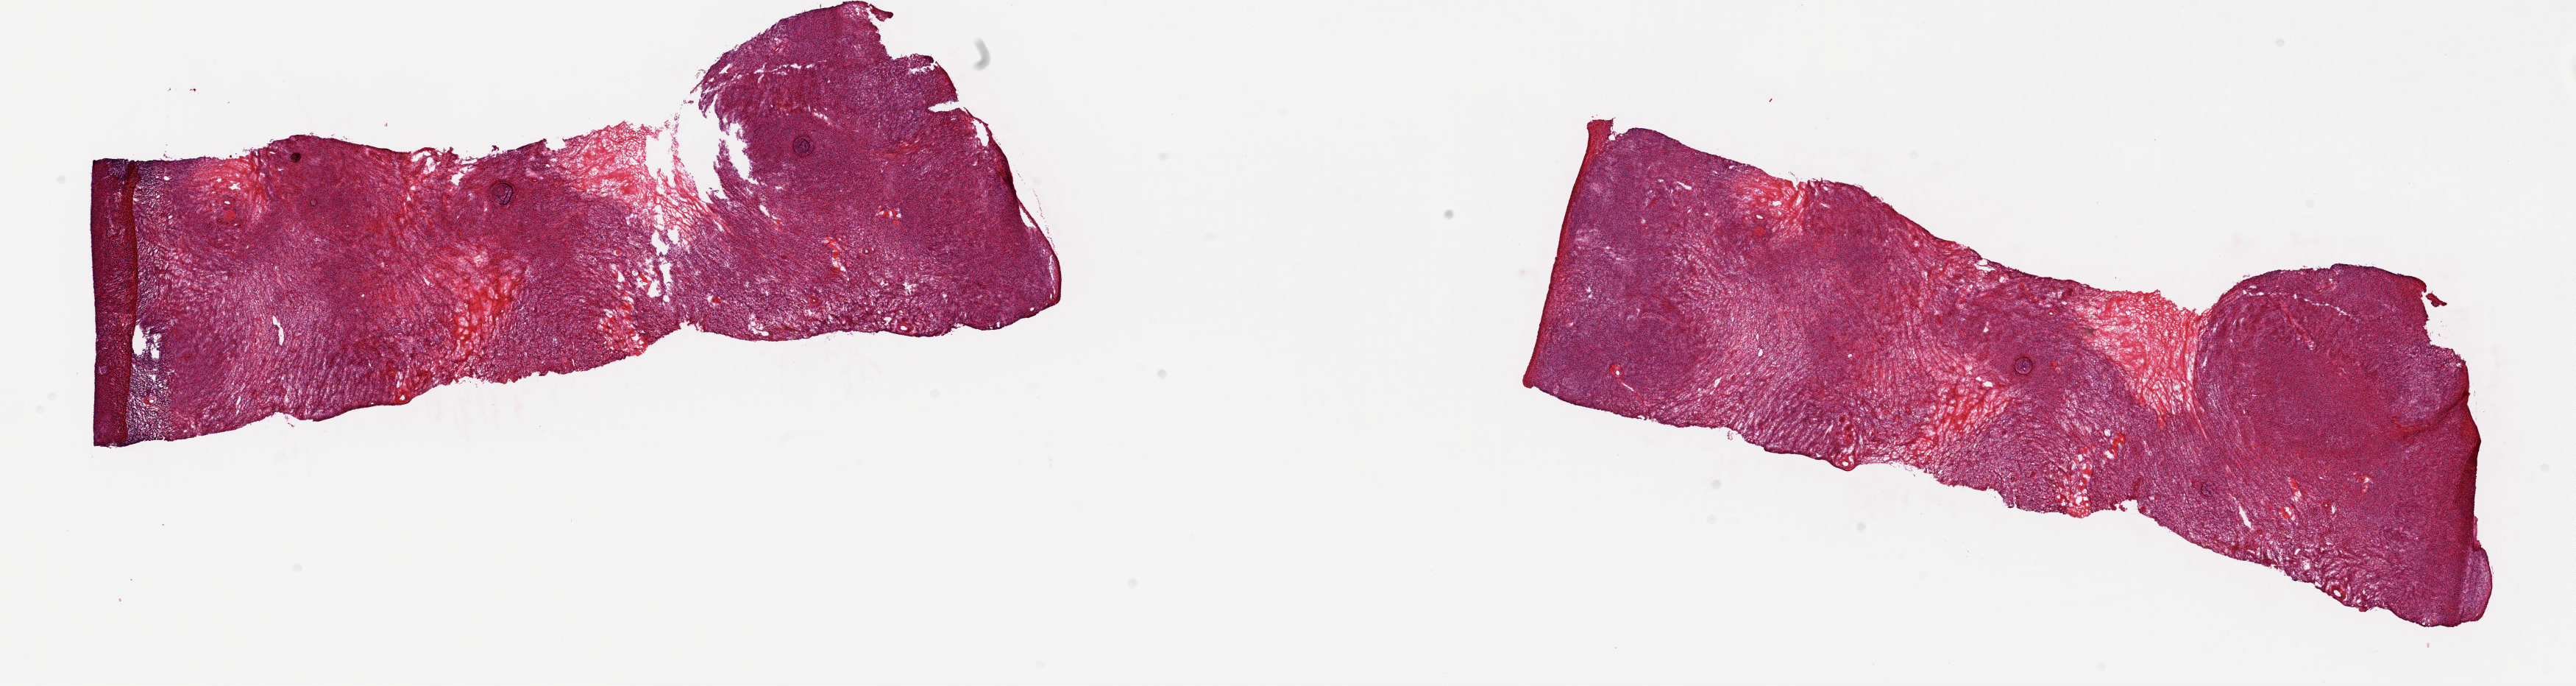
H&E-stained whole-slide image, shown as a low-resolution overview of the whole scanned area (about 27.8 x 7.4 mm); frozen section from the top of the tissue portion; solid tissue normal (non-tumour tissue) sample from the uterus. Female patient; age at initial diagnosis 58 years. Slide review estimates, as recorded: tumour cells 0%, tumour nuclei 0%, normal cells 80%, stromal cells 20%, necrosis 0%. Inflammatory infiltration, as recorded: lymphocyte infiltration 40%, monocyte infiltration 20%, neutrophil infiltration 20%.
- this section: solid tissue normal sample (biorepository sample class)
- patient diagnosis: Endometrioid adenocarcinoma, NOS (endometrium)